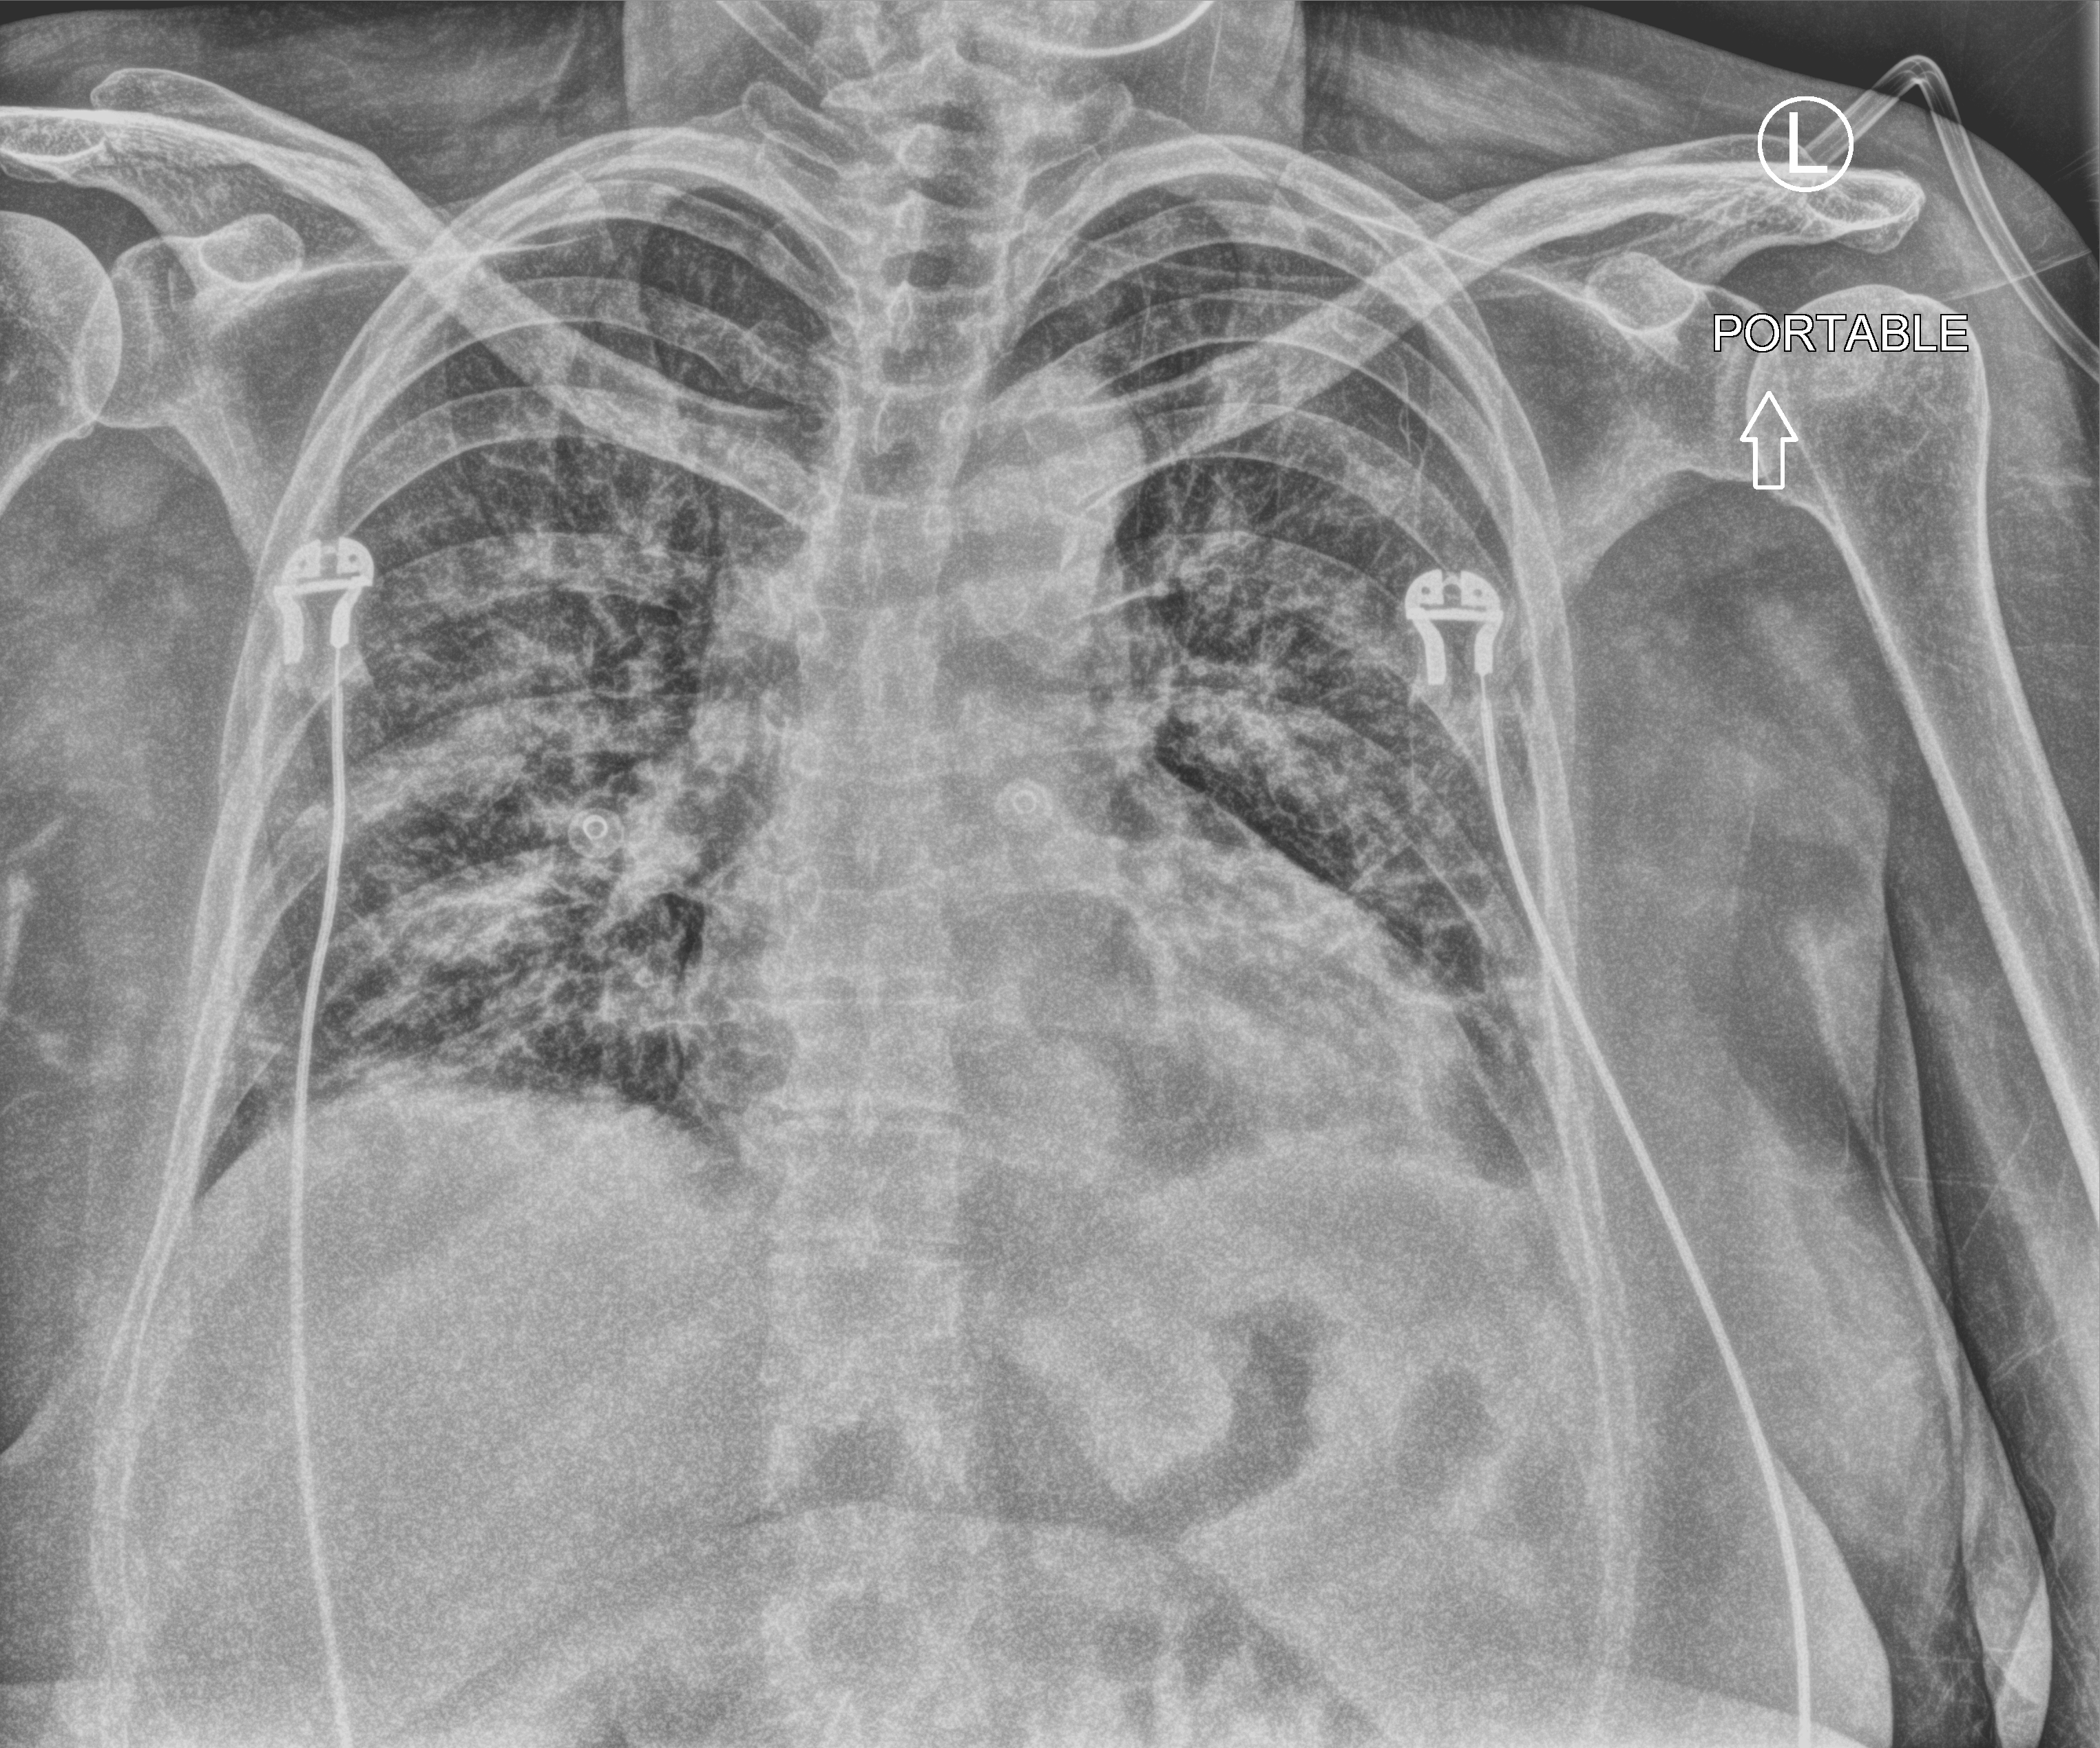
Bedside chest radiograph (computed radiography). Patient hospitalised with COVID-19; female, aged 60–74 years.
Hospital-stay facts (about this admission, not read from this image; timing relative to this image not recorded):
- mechanically ventilated during this hospital stay: no